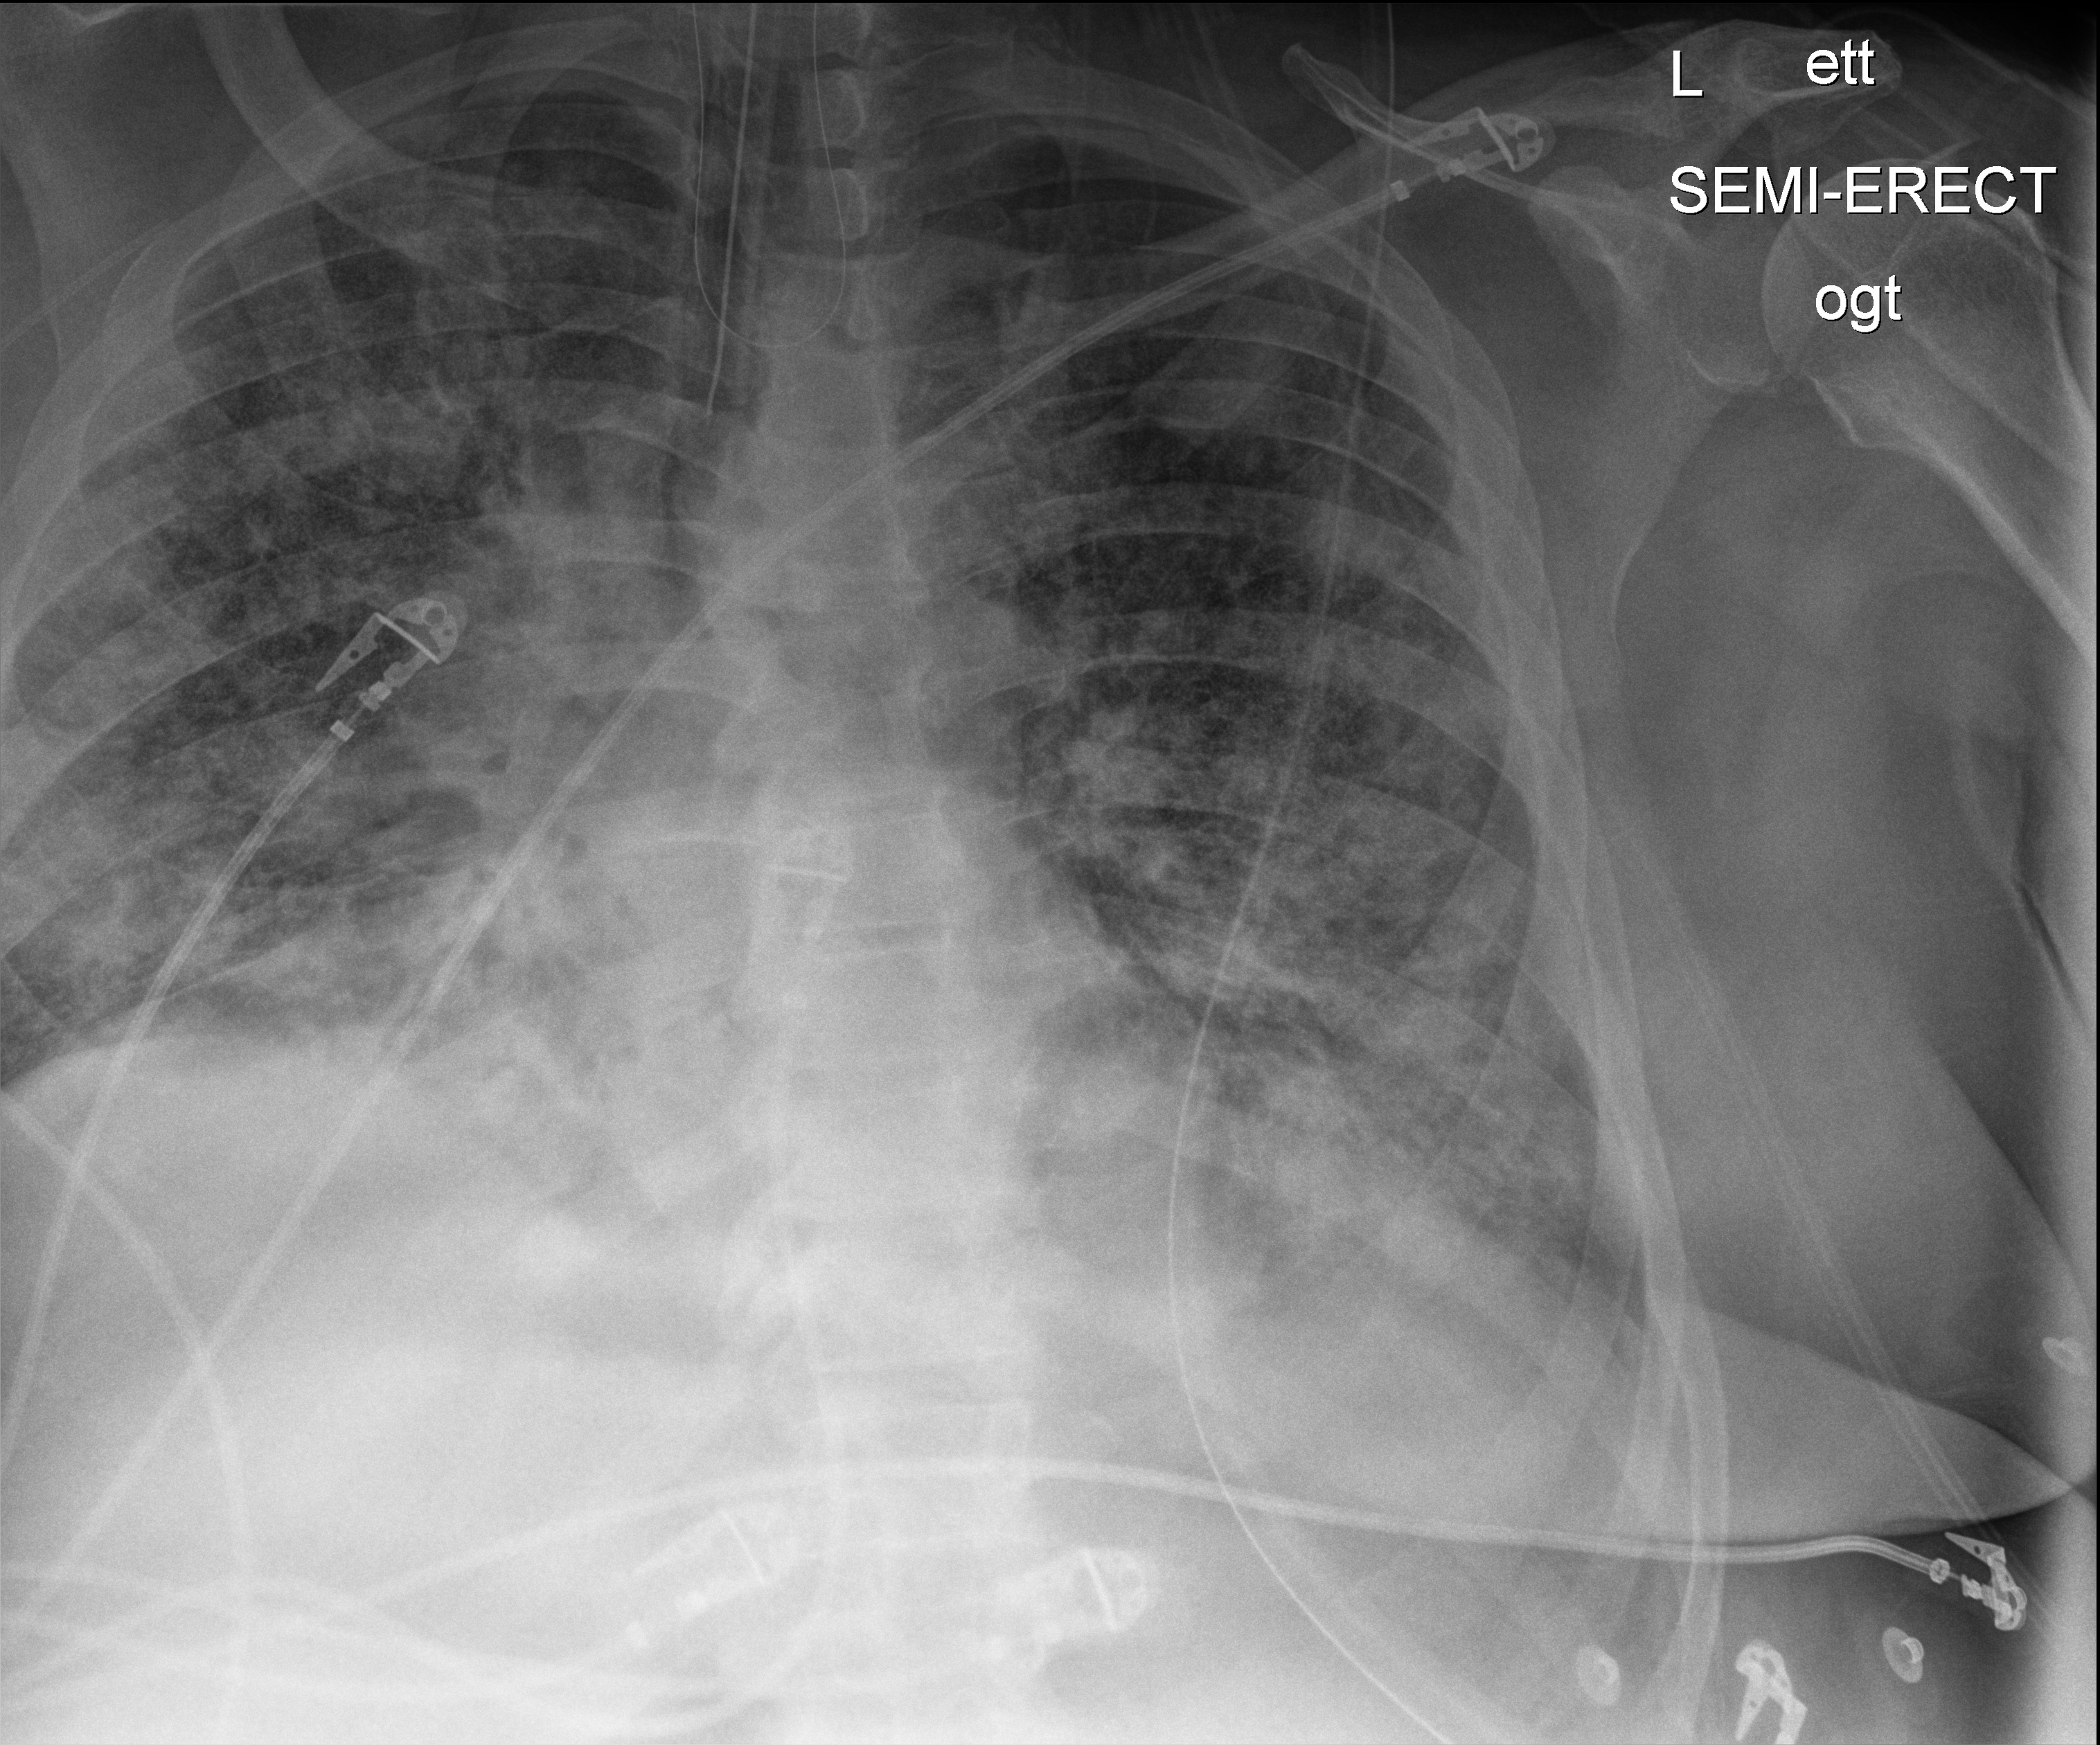
Bedside chest radiograph (digital radiography), anteroposterior (AP) projection. Patient hospitalised with COVID-19; male, aged 60–74 years.
Admission-level facts for this patient (not findings on this image; timing relative to this image not recorded):
- smoking status (admission record): never
- diabetes (admission record): yes
- mechanically ventilated during this hospital stay: yes